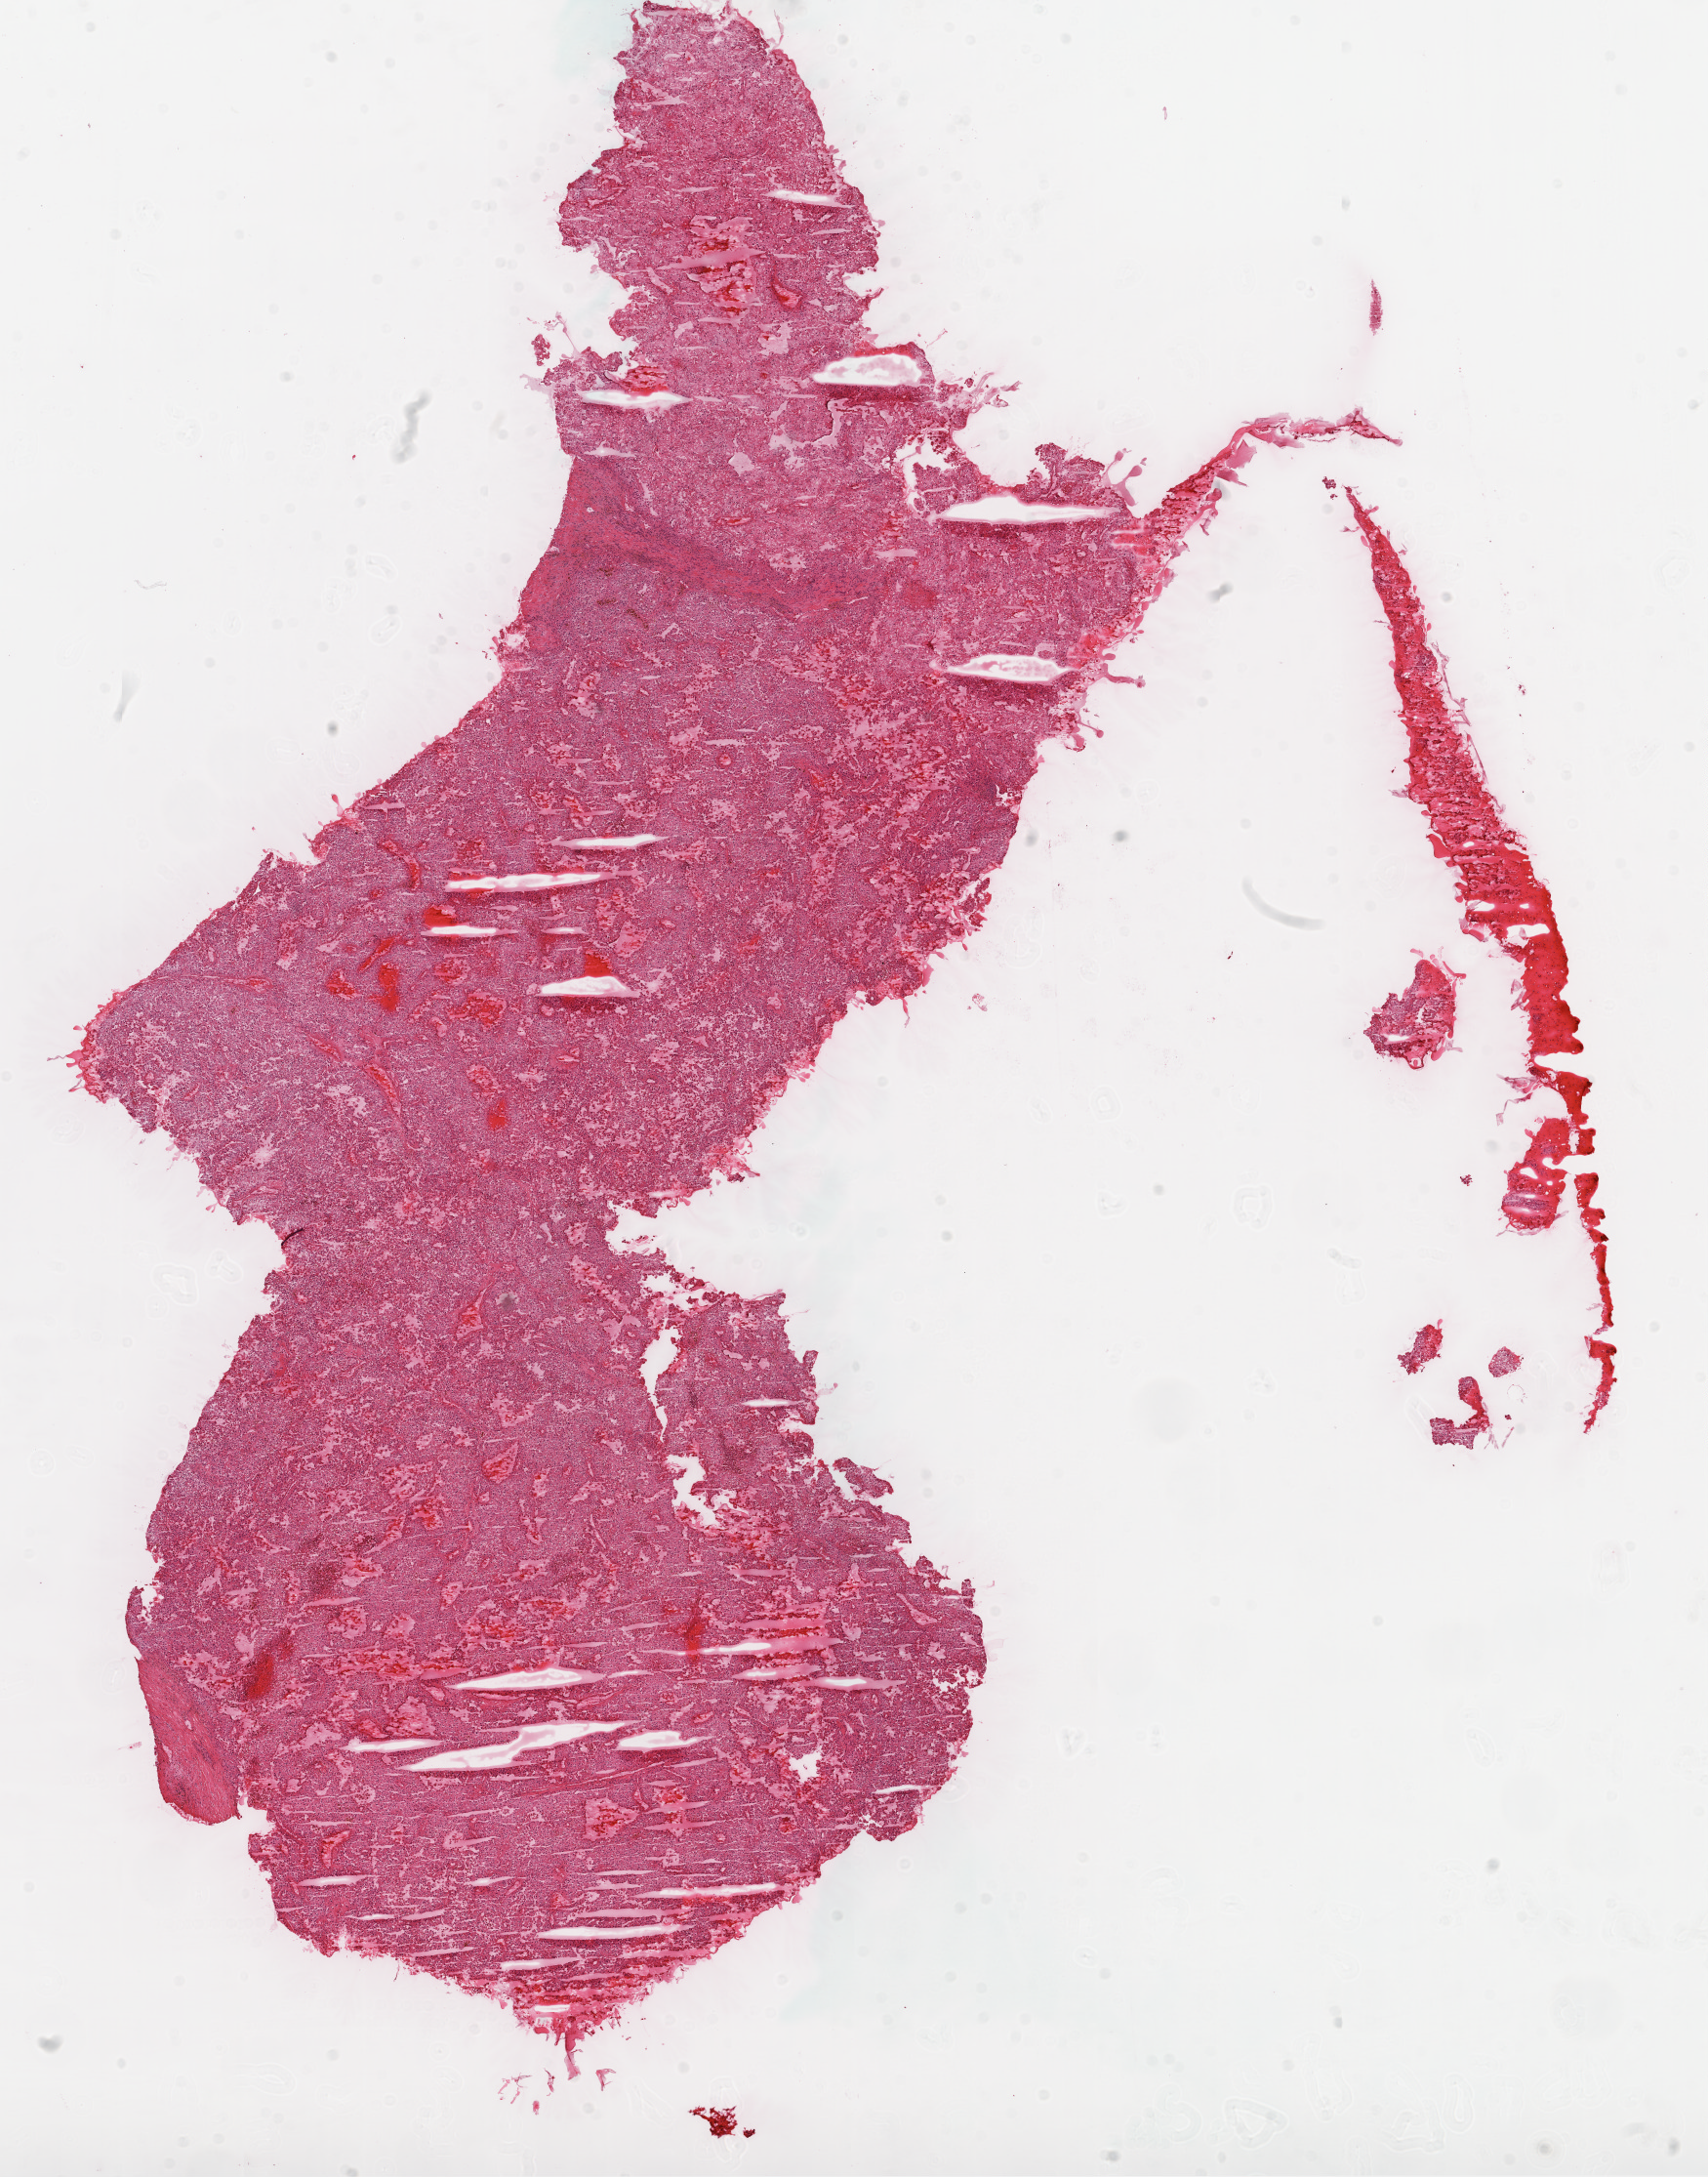
Digitized Hematoxylin and eosin (H&E) stained tissue section (whole slide) — shown as a low-resolution overview of the whole scanned area (about 14.0 x 17.9 mm, acquisition: 20x scan), frozen section from the top of the tissue portion, kidney, primary tumour sample. Male patient; age at initial diagnosis 43 years.
Histologic diagnosis: Clear cell adenocarcinoma, NOS.